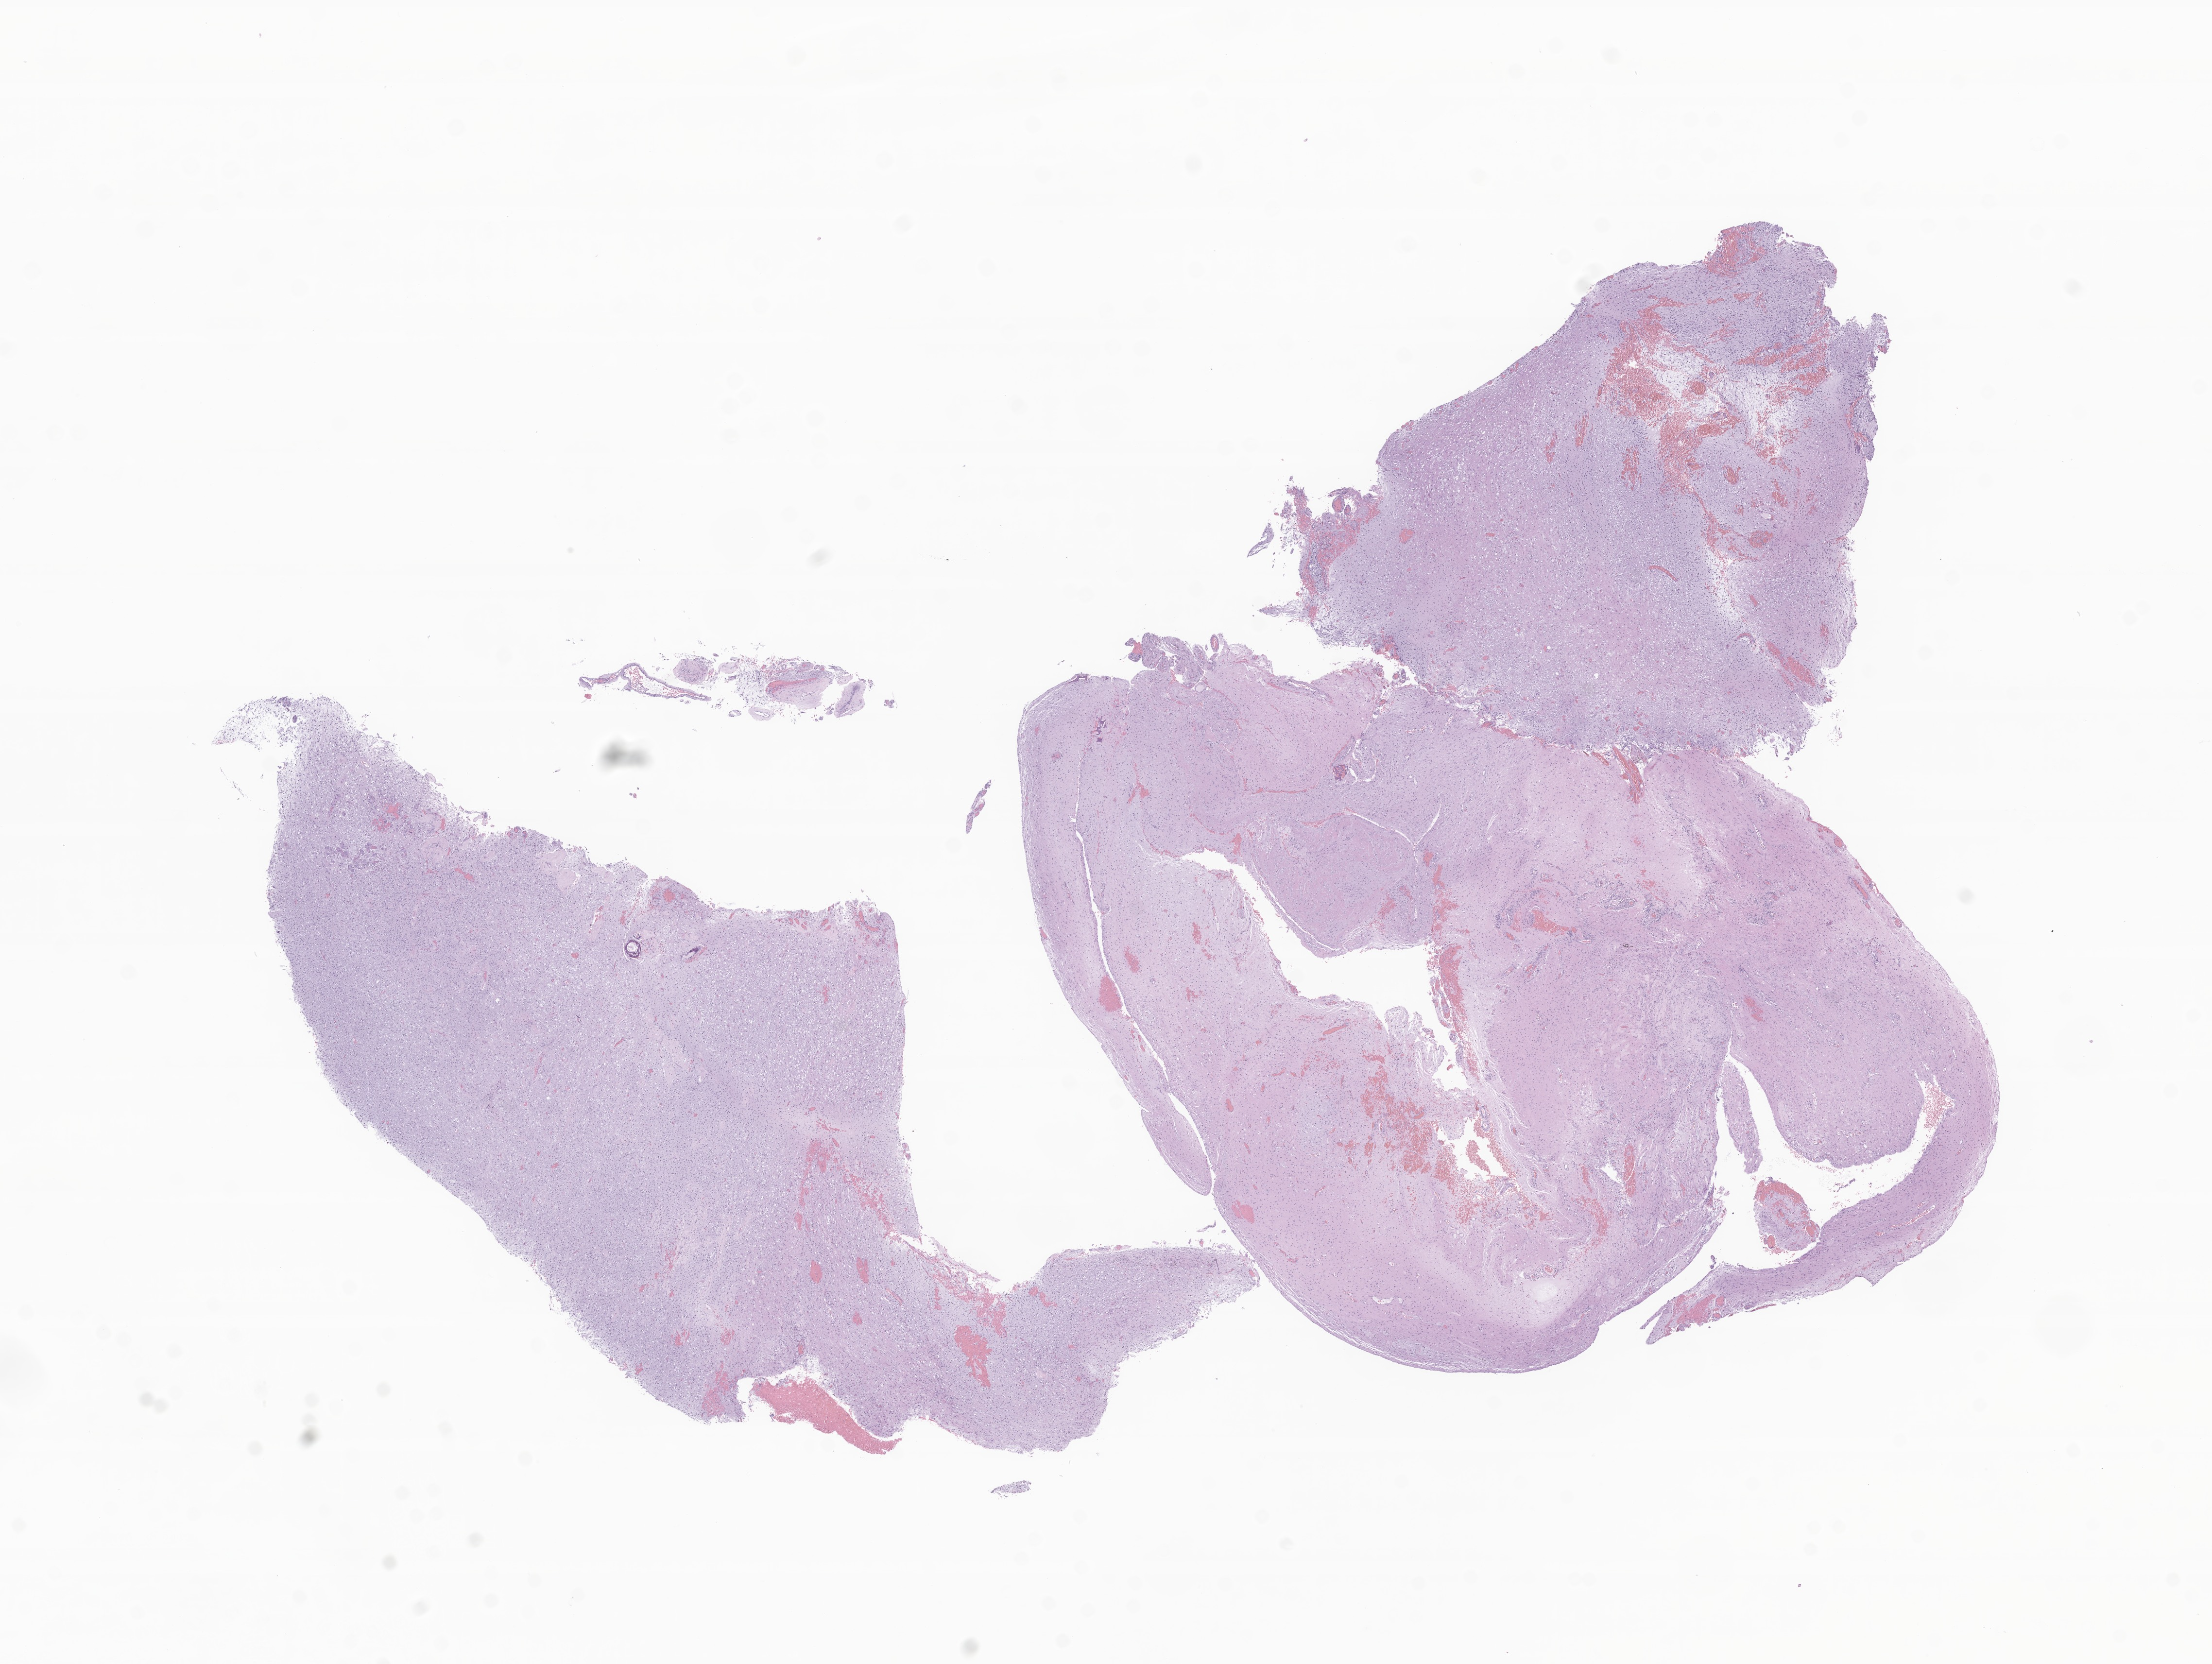
H&E whole-slide image of tumor tissue from the spinal cord, shown as a low-resolution overview of the whole scanned area (about 19.2 x 14.4 mm), FFPE section. Patient male; age 197 months (16 years 5 months).
Diagnosis: Pilocytic astrocytoma.